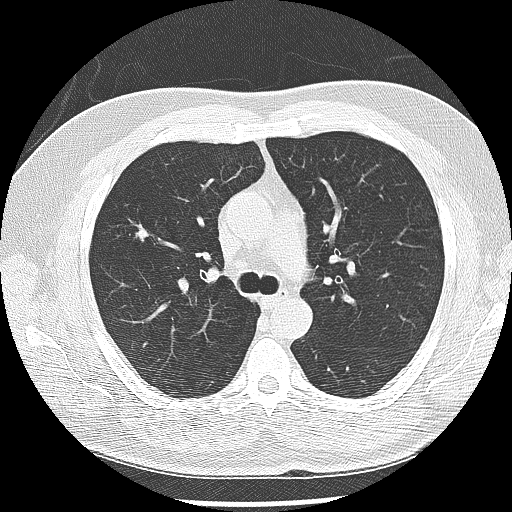
Low-dose screening chest CT, one axial slice. Position 177 of 265 along the scan axis. Reconstruction kernel LUNG. 120 kVp. Lung window (W 1500 / L -600 HU). 2.5 mm slice thickness. 512 × 512 image matrix, field of view 340 × 340 mm.
Annotated regions visible in this slice (outlined manually by an expert reader):
- lesion 1 (tumor, upper lobe of right lung): bounding box [x1, y1, x2, y2] px = [136, 224, 150, 242]